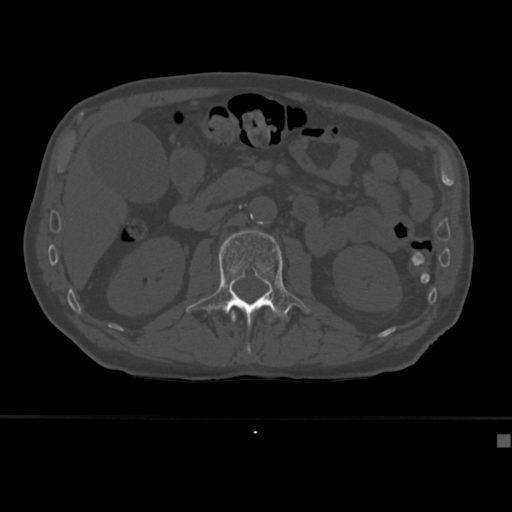
CT including the spine, one axial slice; slice 151 of 430 in the series (ordered by position); reconstruction kernel Br40s; 120 kVp; bone window (W 1800 / L 400 HU); 512 × 512 image matrix. Patient: male, 64 years. Case-level facts recorded for this patient, not image findings: primary cancer: uterus; vertebrae with lytic lesions (as recorded): T1, T4, T5, T7, L5.
Outlined on this slice (semi-automatic segmentation, software-assisted and operator-edited):
- L1 vertebra: bounding box [x1, y1, x2, y2] px = [231, 309, 275, 354]
- L2 vertebra: [186, 229, 310, 329]